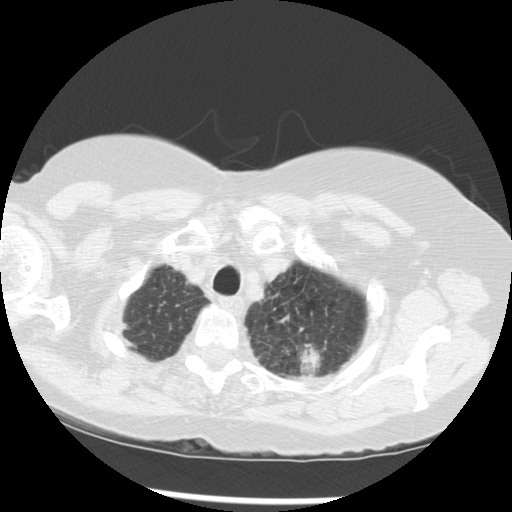
Low-dose screening chest CT, one axial slice; position 248 of 283 along the scan axis; reconstruction kernel STANDARD; 120 kVp; lung window (W 1500 / L -600 HU); 2.5 mm slice thickness; 512 × 512 image matrix, field of view 330 × 330 mm.
Outlined on this slice (manually delineated by an expert):
- lesion 1 (tumor, upper lobe of left lung): box from (x=300, y=344) to (x=322, y=375) px